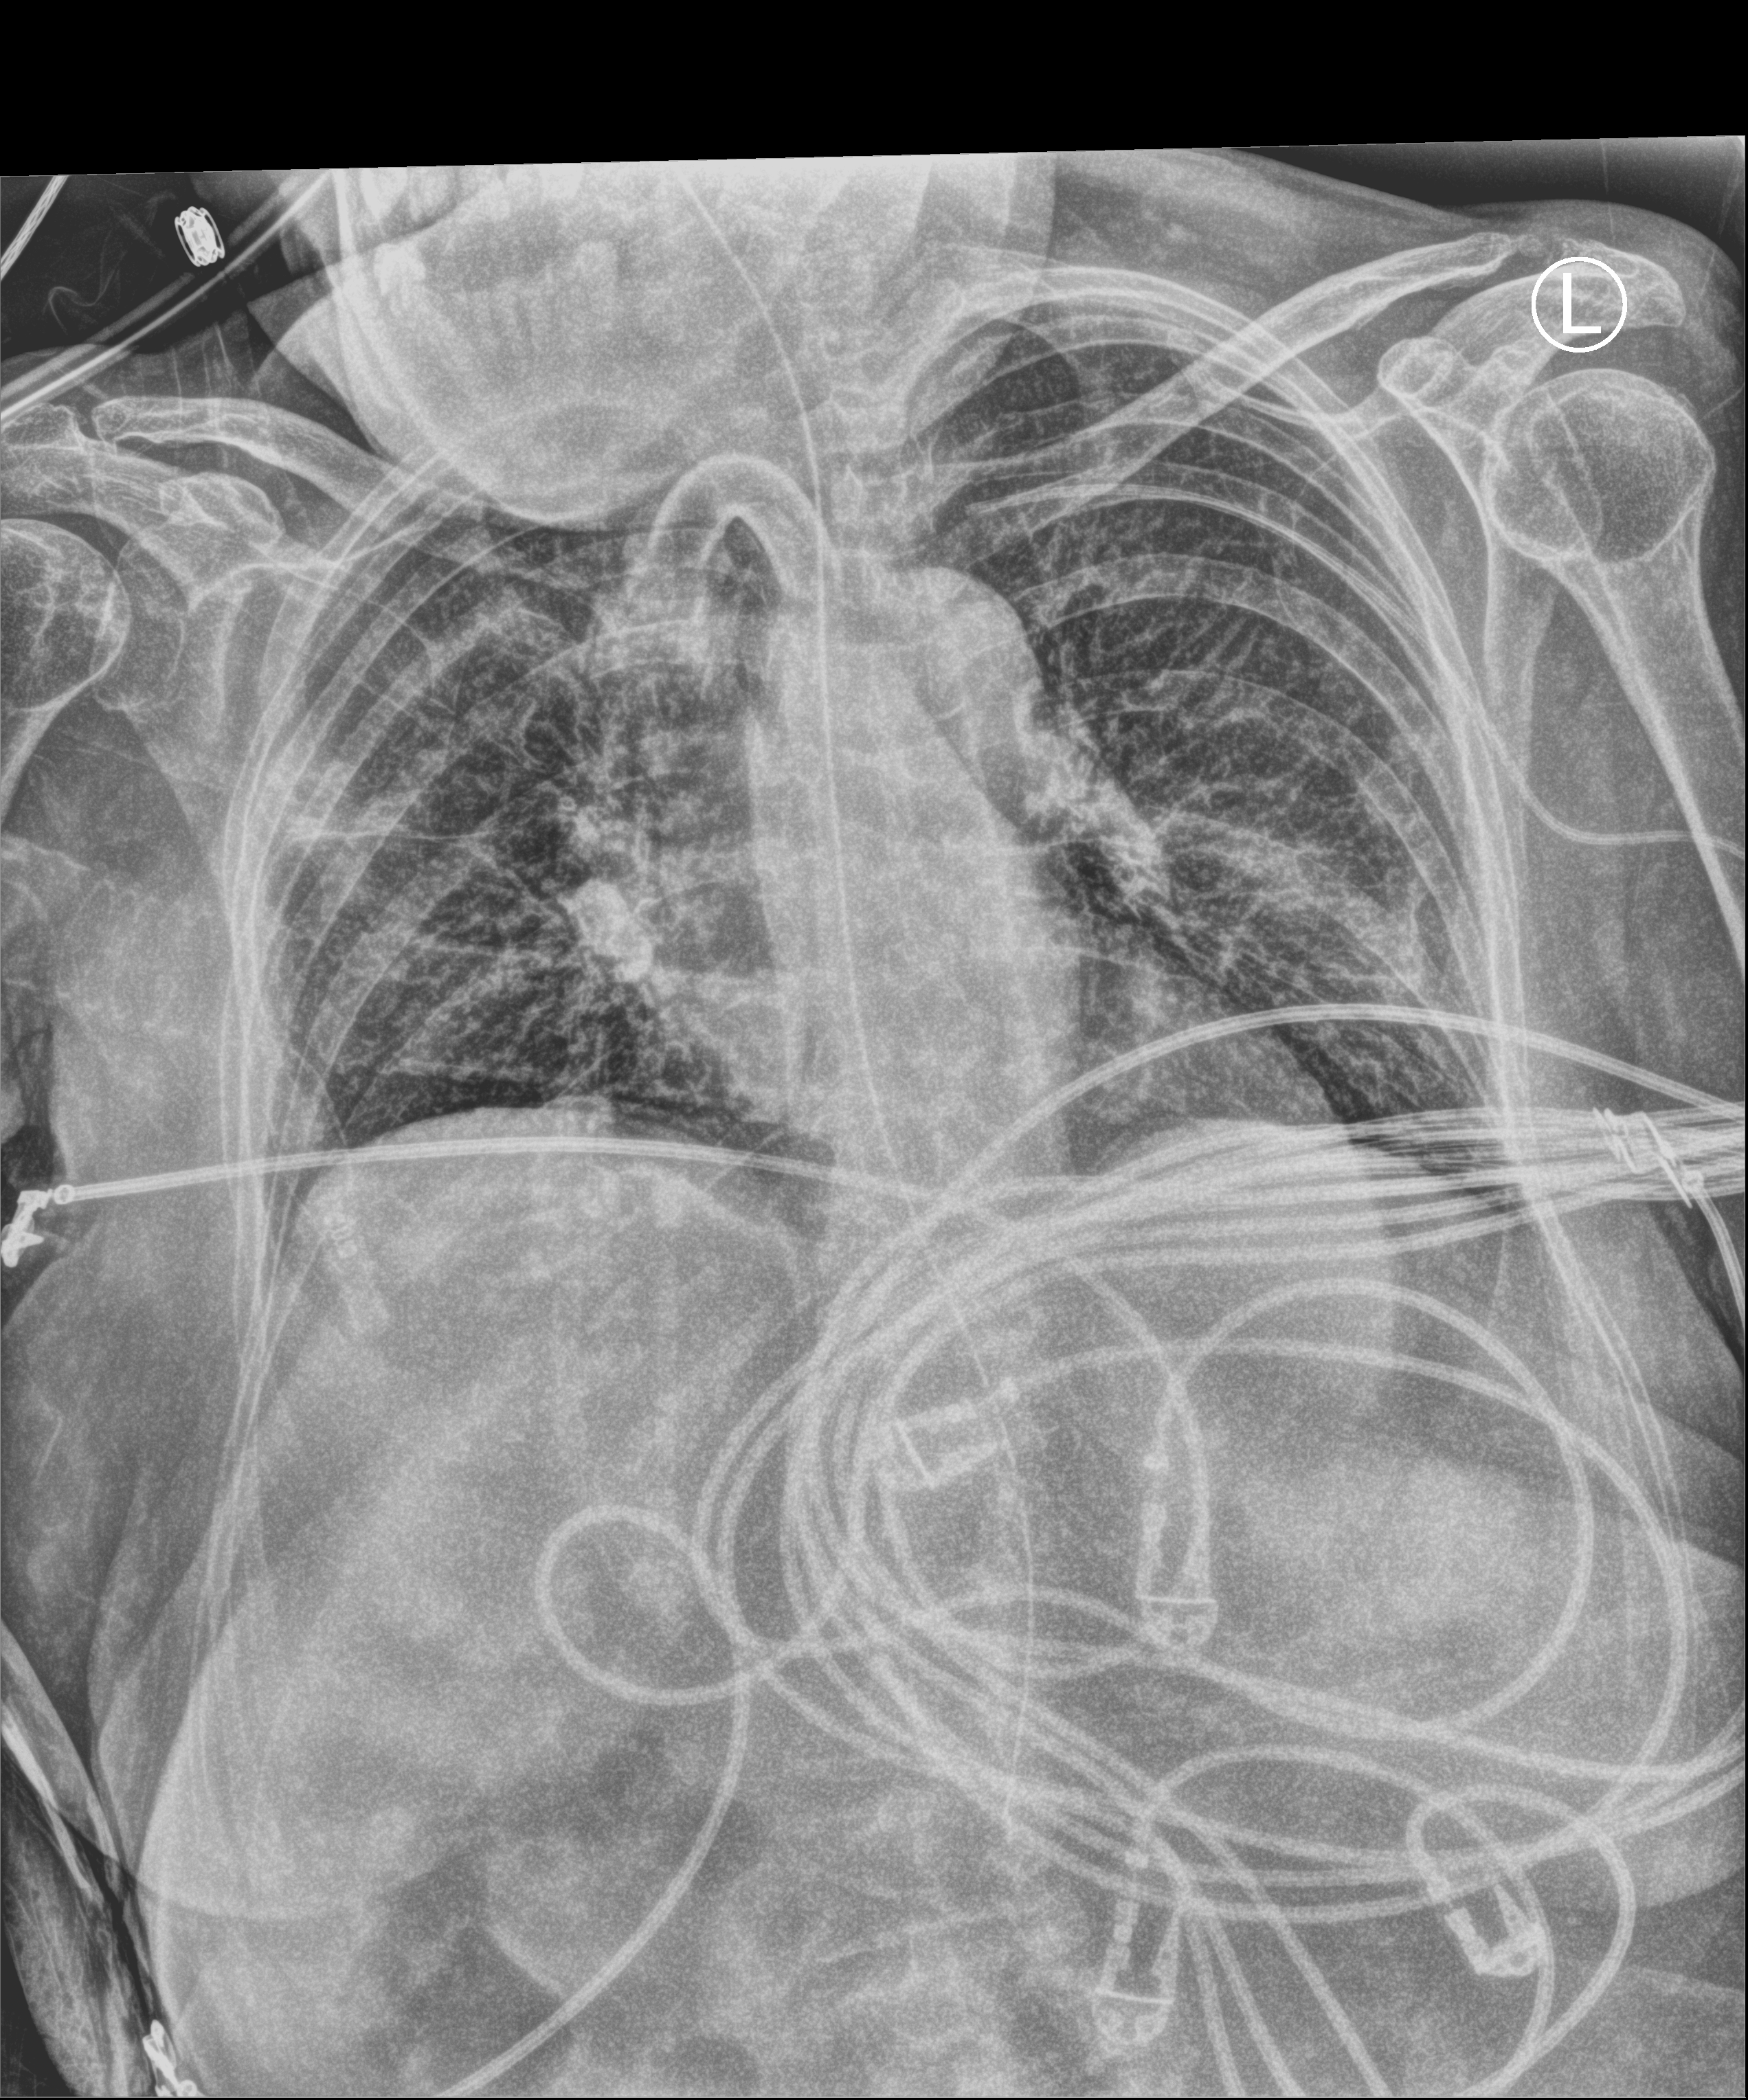
Portable chest radiograph, anteroposterior (AP) projection. Female patient hospitalised with COVID-19, age 75–90 years.
From the hospital-stay record, not from the radiograph (when in the stay this image was taken is not recorded): mechanically ventilated during this hospital stay: yes; admitted to intensive care during this hospital stay: yes.